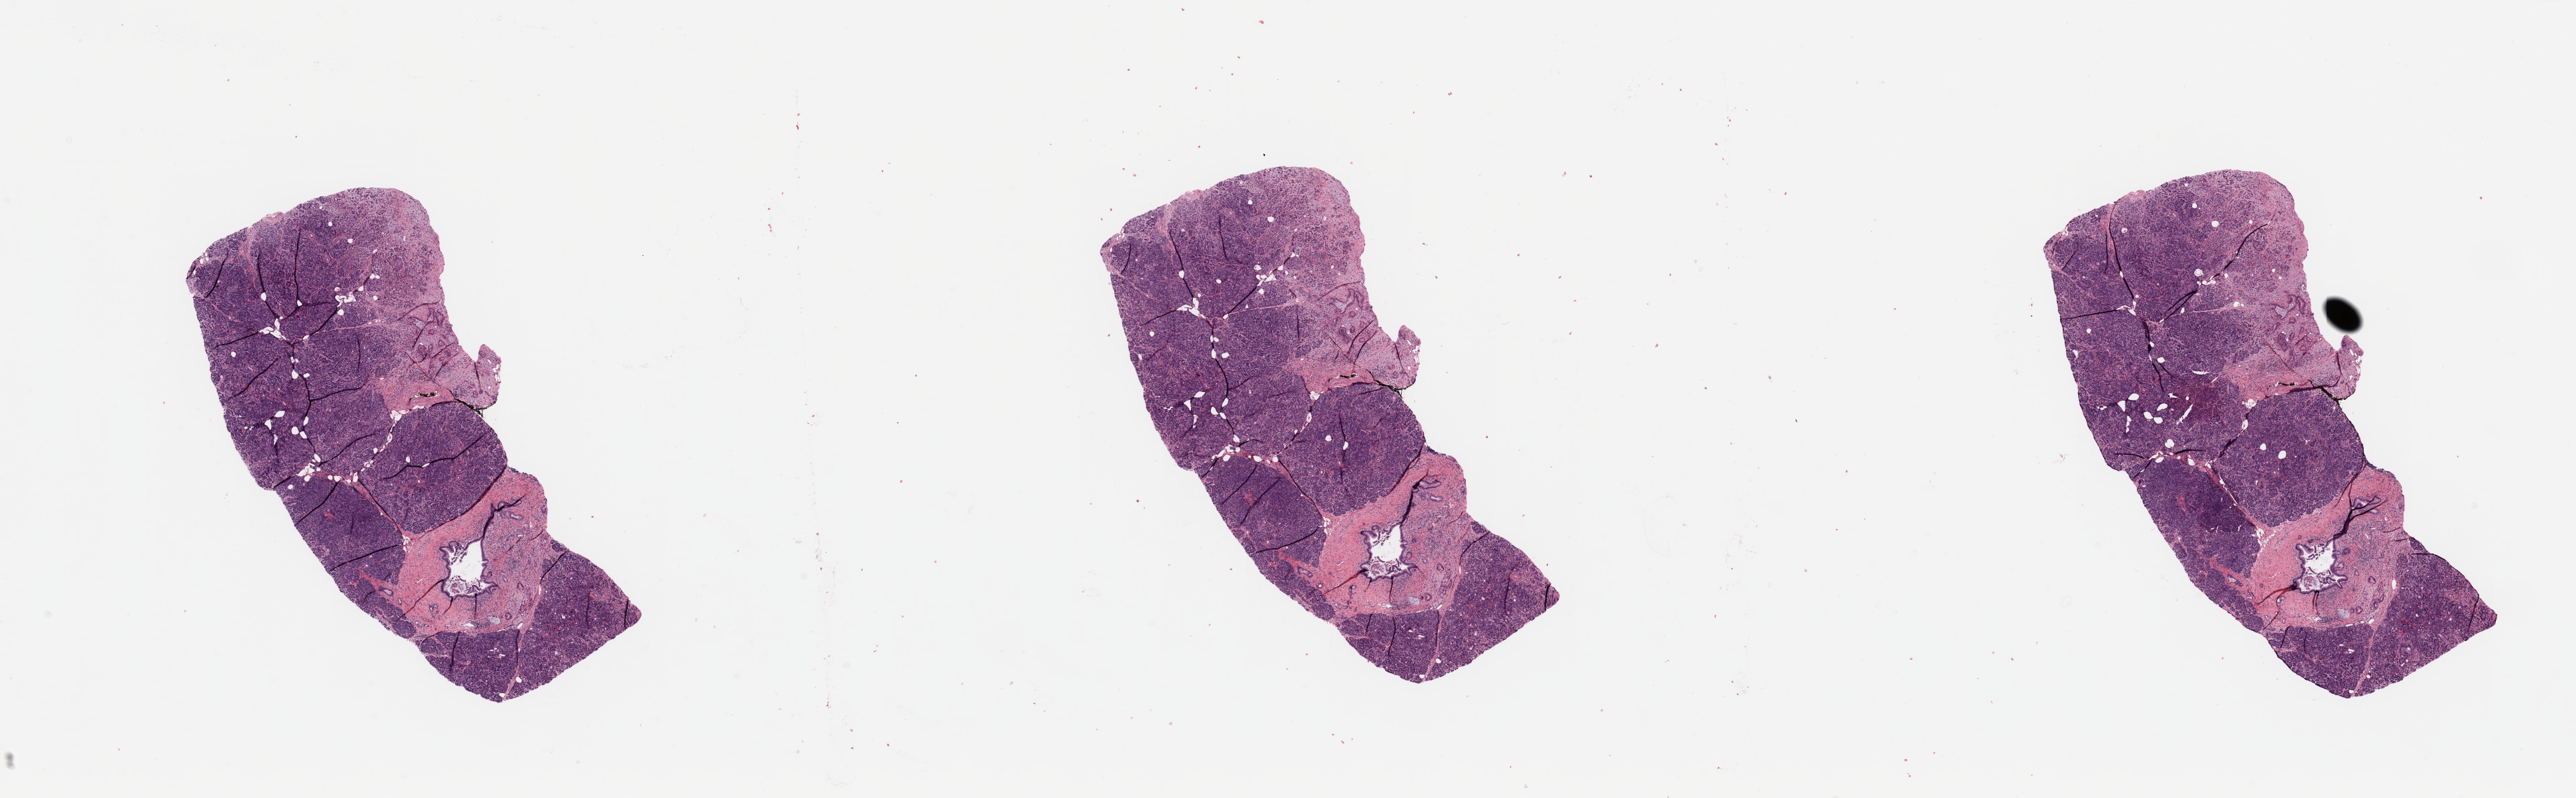
Hematoxylin and eosin (H&E) stained whole-slide image, a low-resolution overview of the entire scanned area, about 30.5 x 9.5 mm (acquisition: 20x scan); normal (non-tumour) tissue sample, sampled site: pancreas. Male, 72 y/o.
- this section: normal (non-tumour) tissue from the same patient
- patient diagnosis: Infiltrating duct carcinoma, NOS